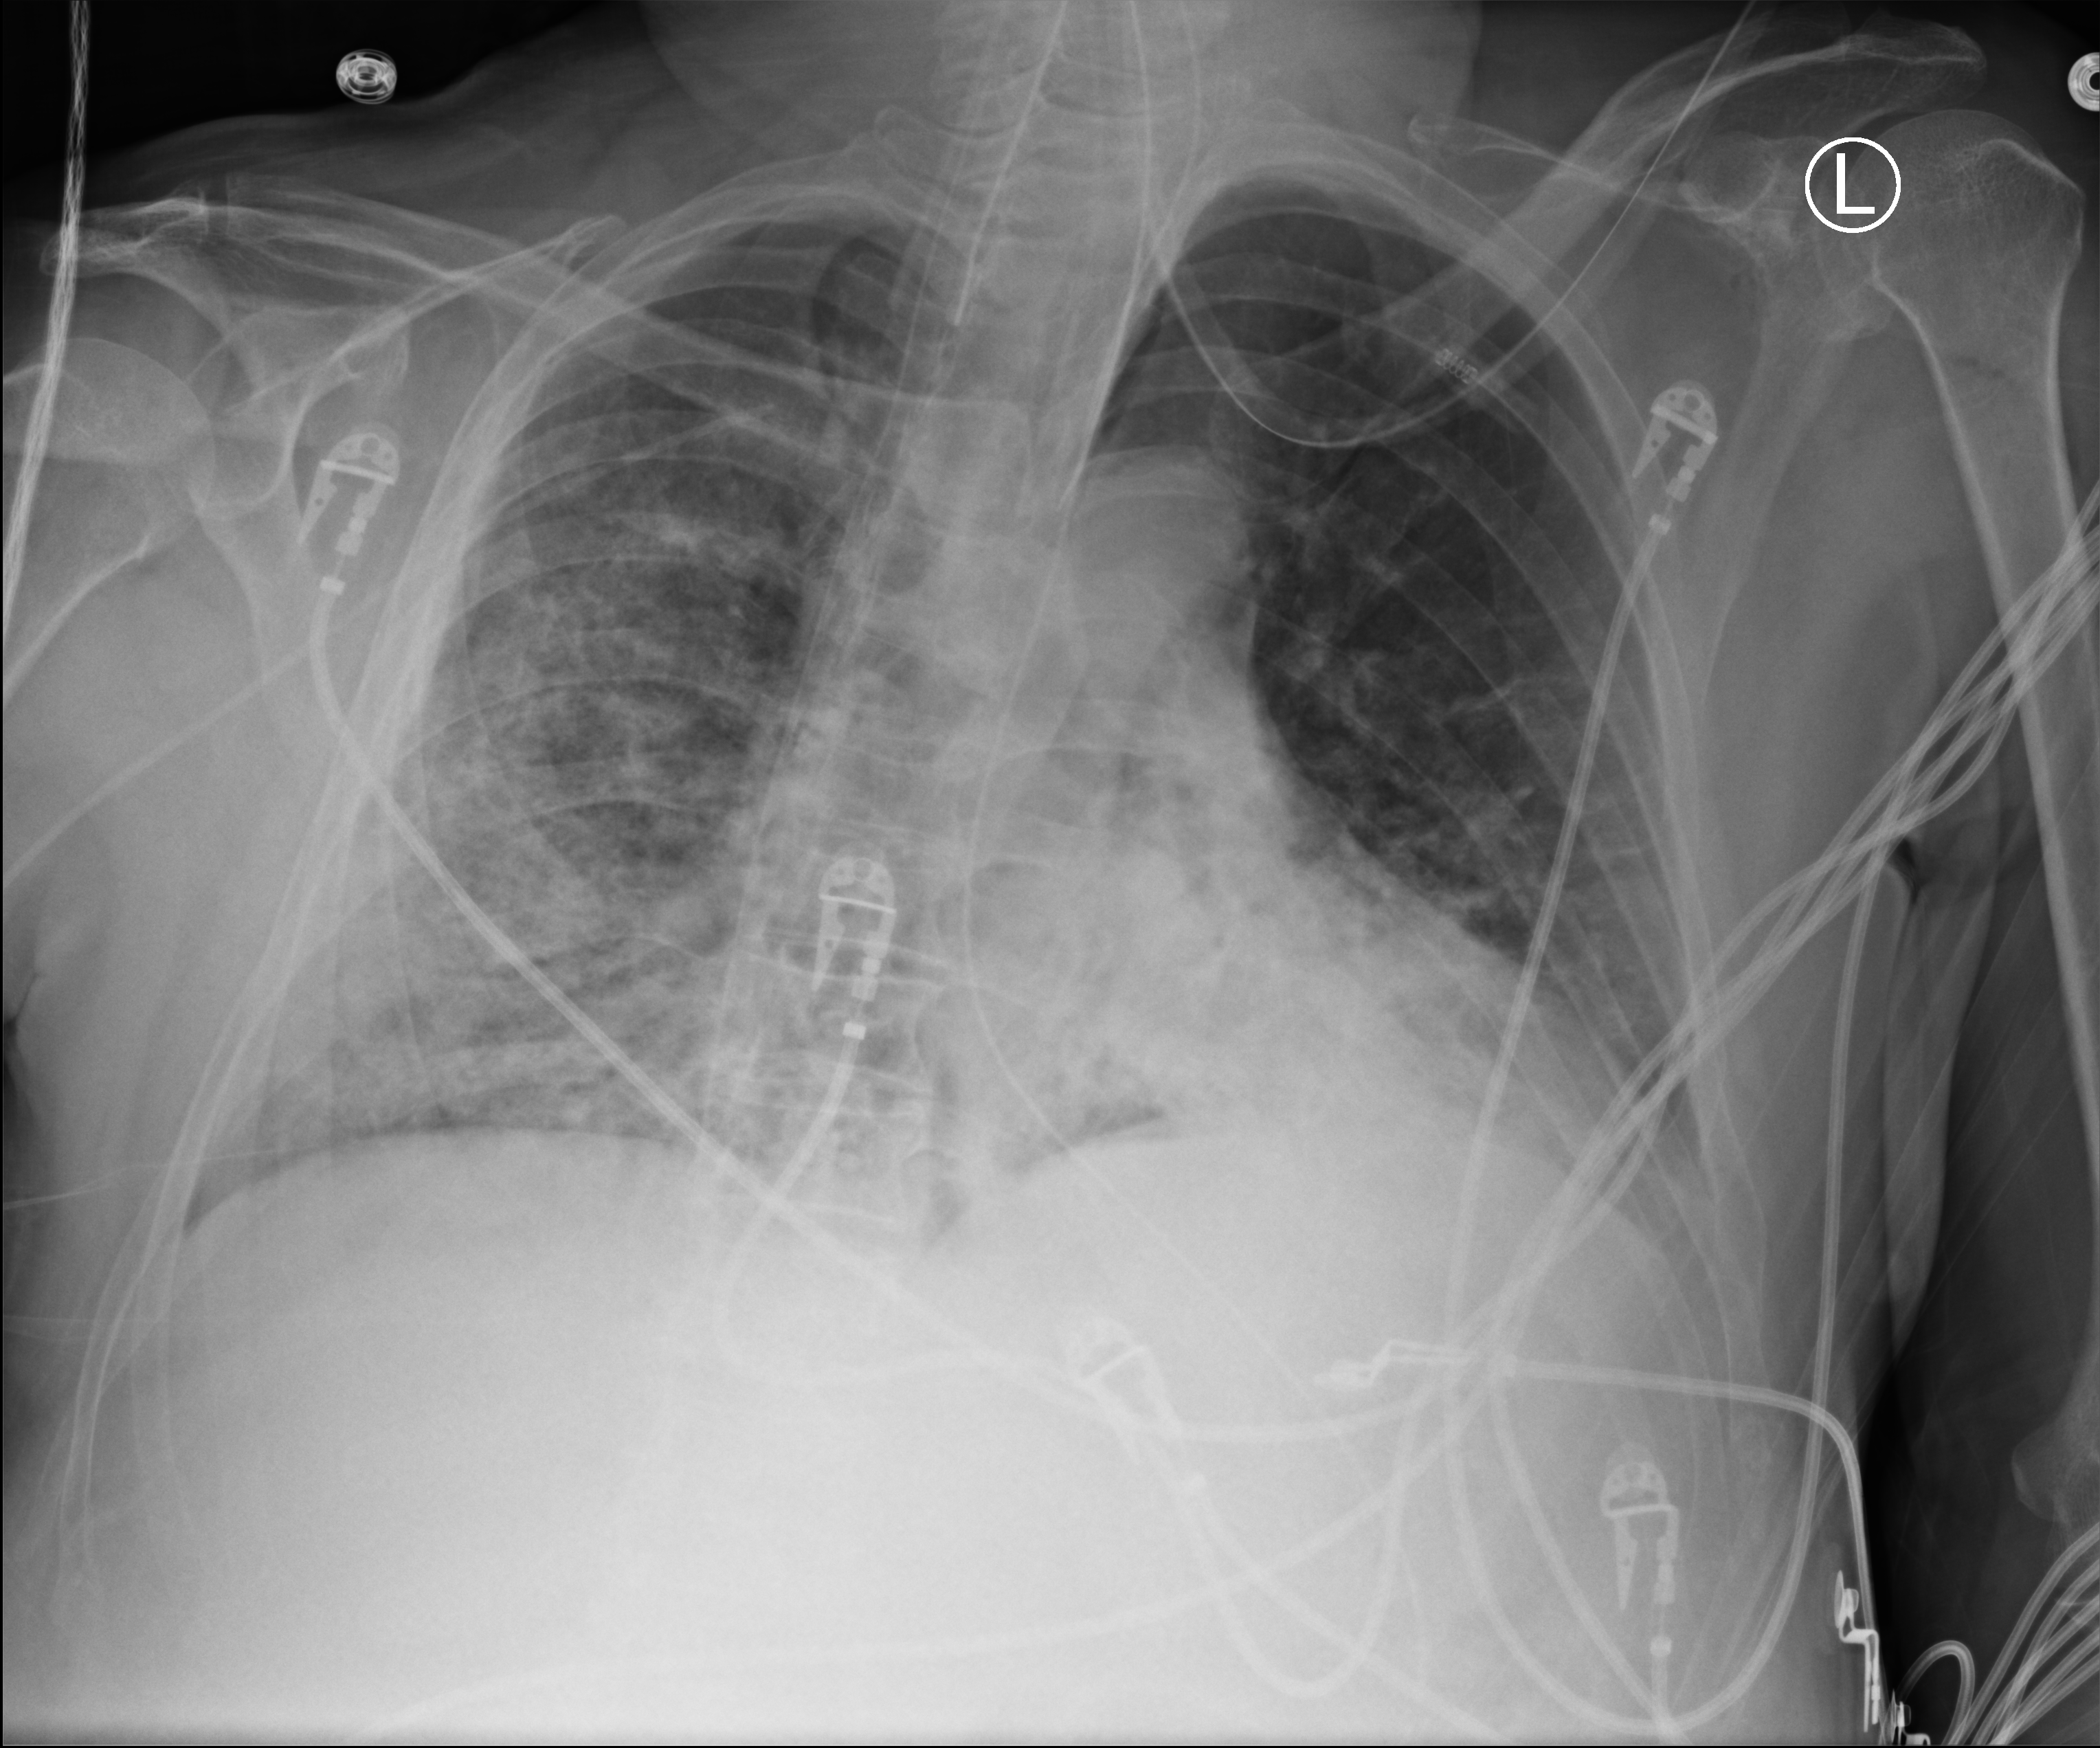
Bedside chest radiograph (computed radiography), anteroposterior (AP) projection. Patient hospitalised with COVID-19; male, aged 60–74 years.
From the hospital-stay record, not from the radiograph (when in the stay this image was taken is not recorded): admitted to intensive care during this hospital stay: yes; smoking status (admission record): never; length of hospital stay: 19 days.